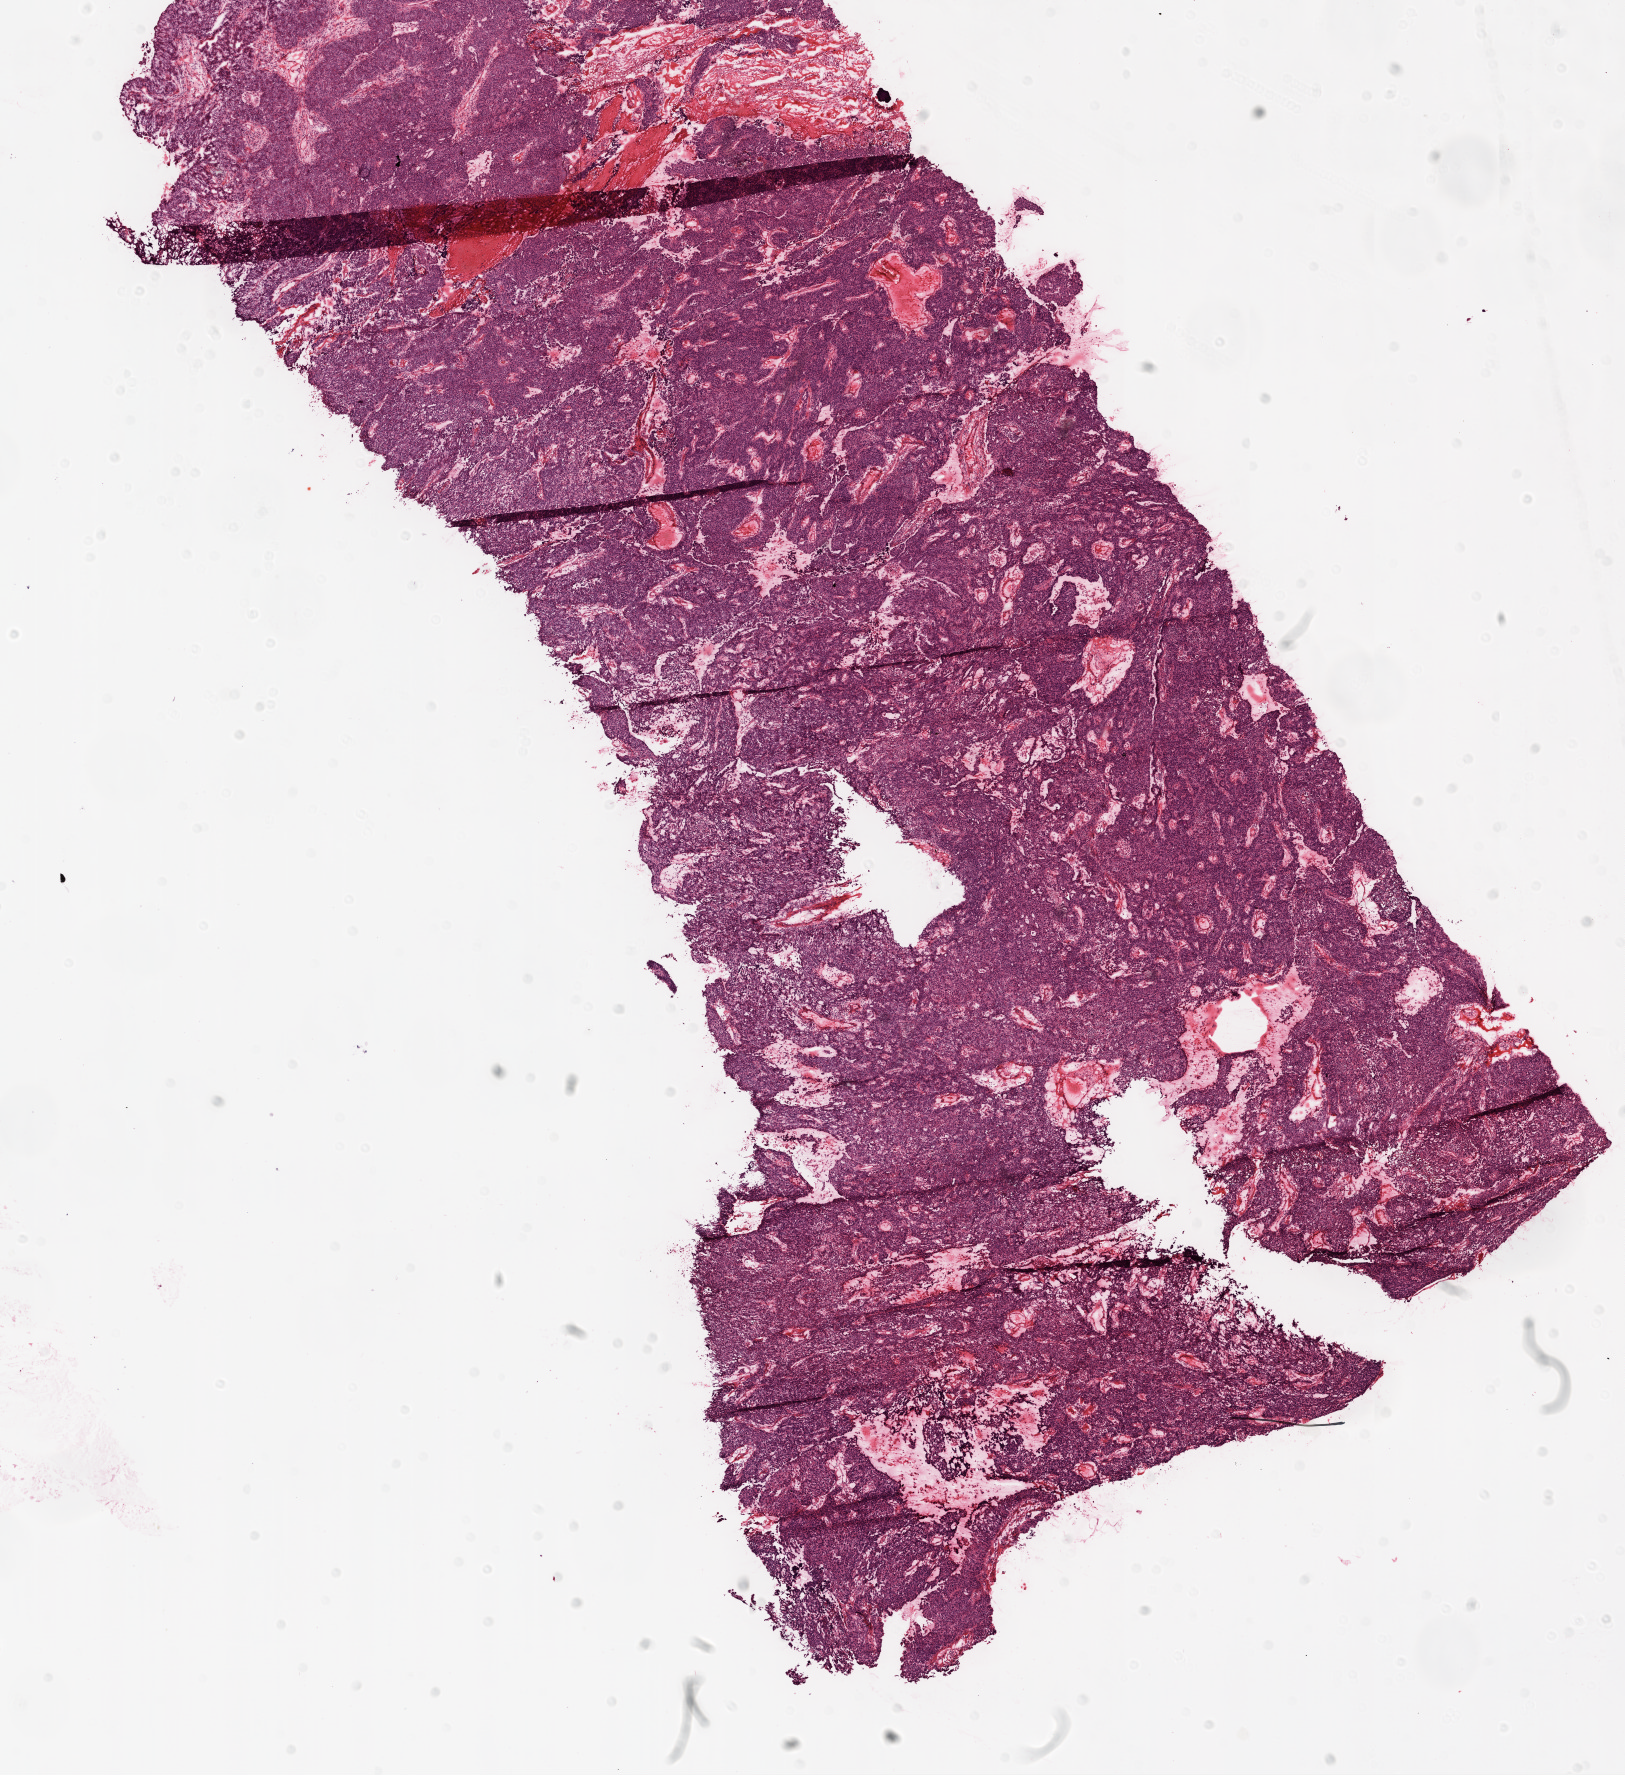
Whole-slide histology image, H&E-stained, shown as a low-resolution overview of the whole scanned area (about 13.0 x 14.2 mm, acquisition: 20x scan); frozen section from the top of the tissue portion; primary tumour sample from the ovary. Female patient; age at initial diagnosis 63 years. Histologic grade: G3 (poorly differentiated). Pathologist review of this section (percent, as recorded): tumour cells 94%, tumour nuclei 95%, normal cells 0%, stromal cells 5%, necrosis 1%.
Pathologic diagnosis: Serous cystadenocarcinoma, NOS. Laterality: bilateral. FIGO stage: IIIC.